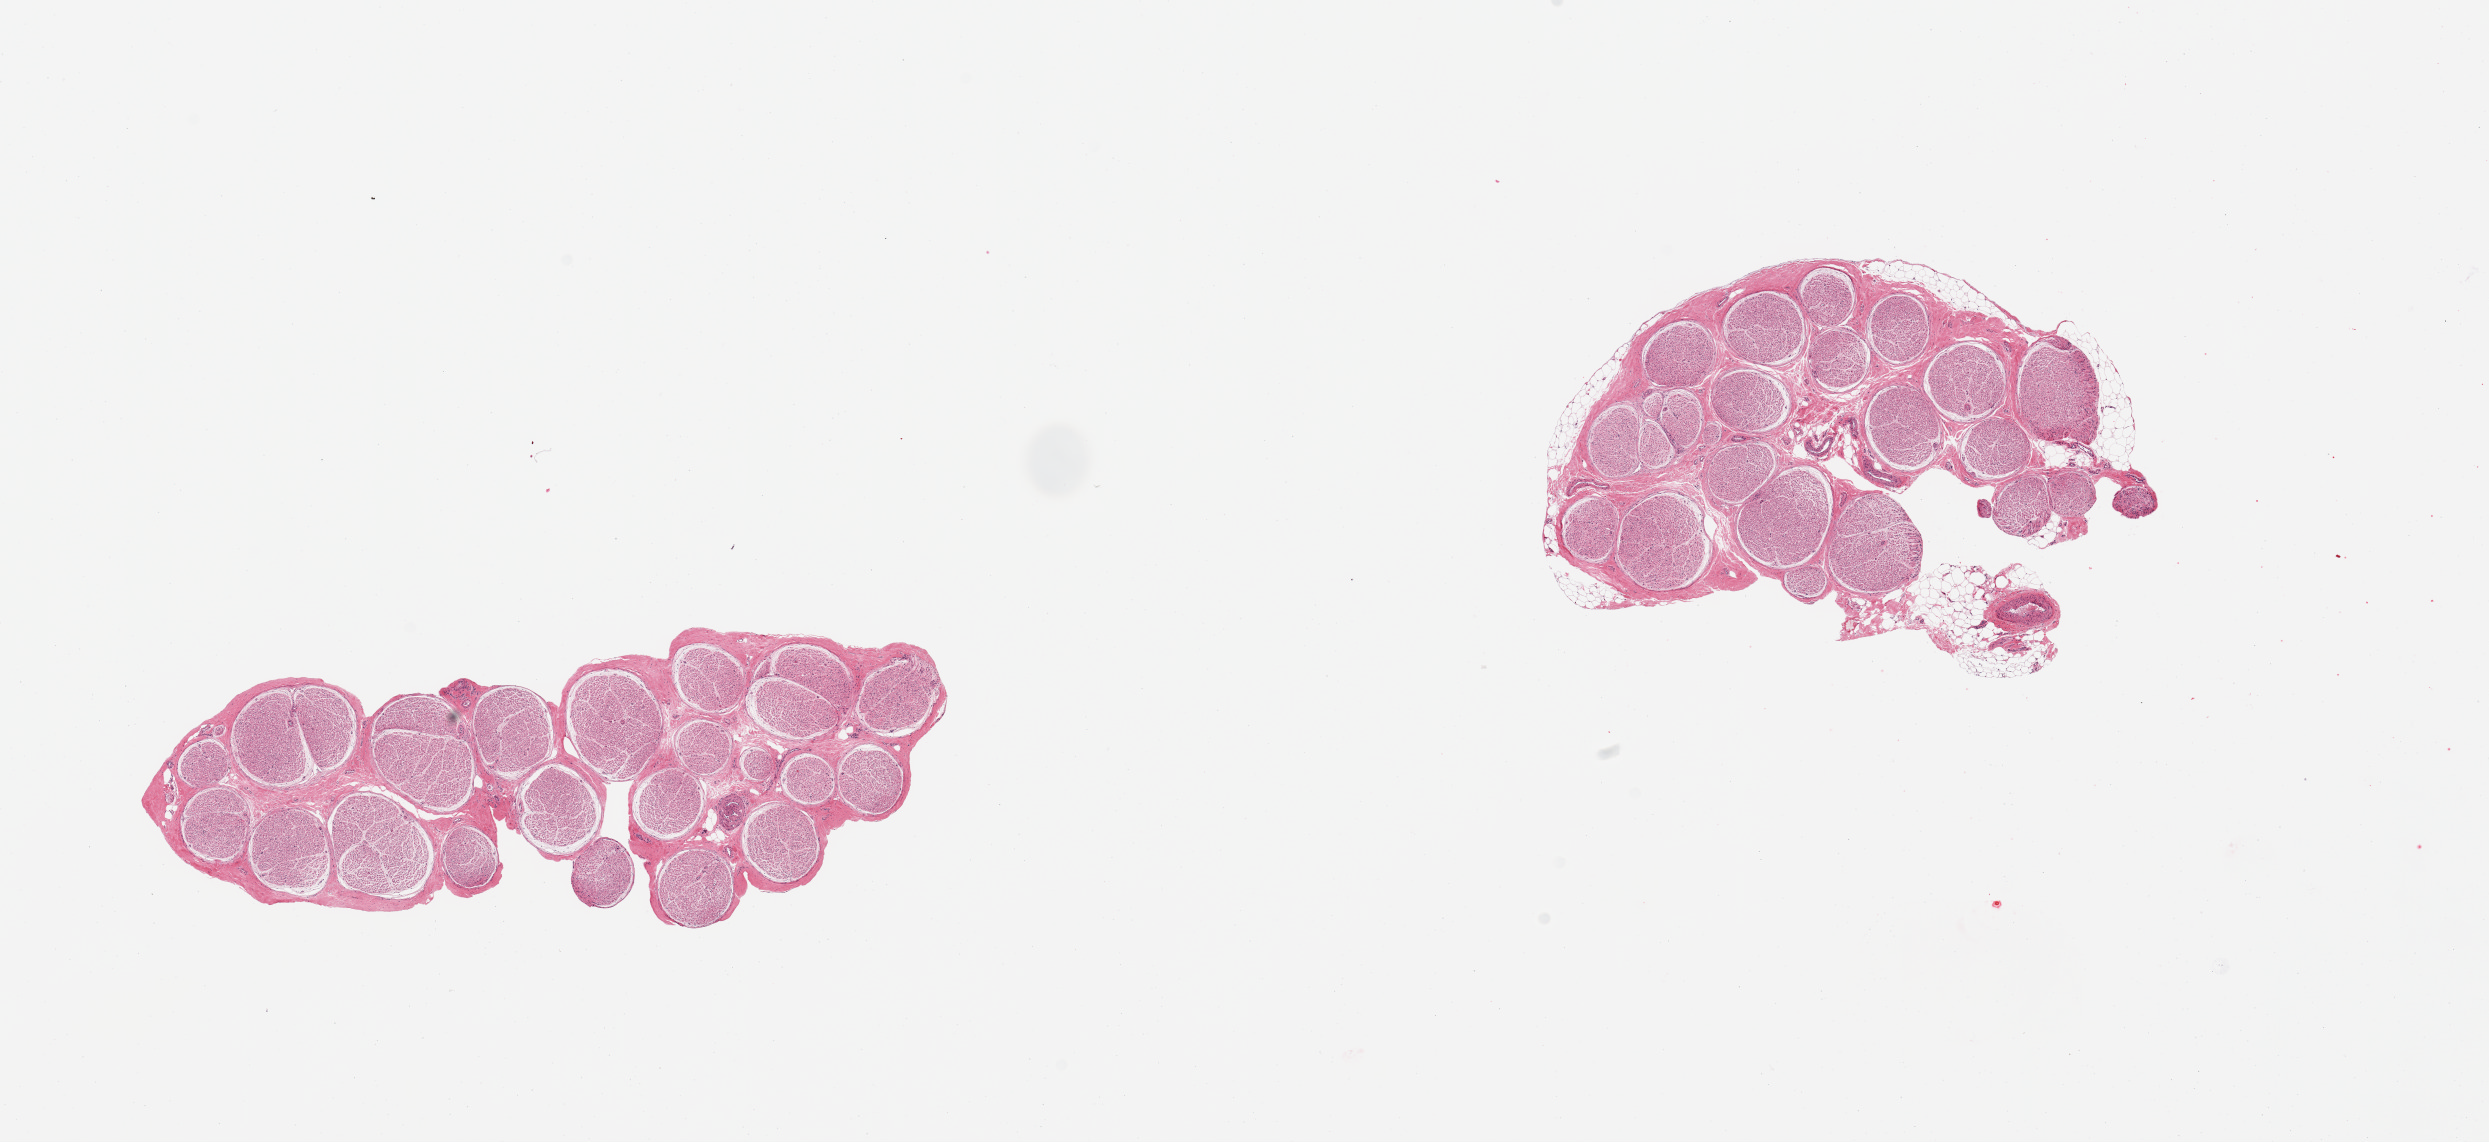
H&E whole-slide image, brightfield, low-resolution overview of the scanned area, about 19.7 x 9.0 mm; PAXgene-fixed paraffin-embedded (PFPE) section; target tissue: tibial nerve; donor tissue sample. Donor sex: female.
- pathologist's review note for this sample: 2 pieces; 5% external fat on 1, none on other